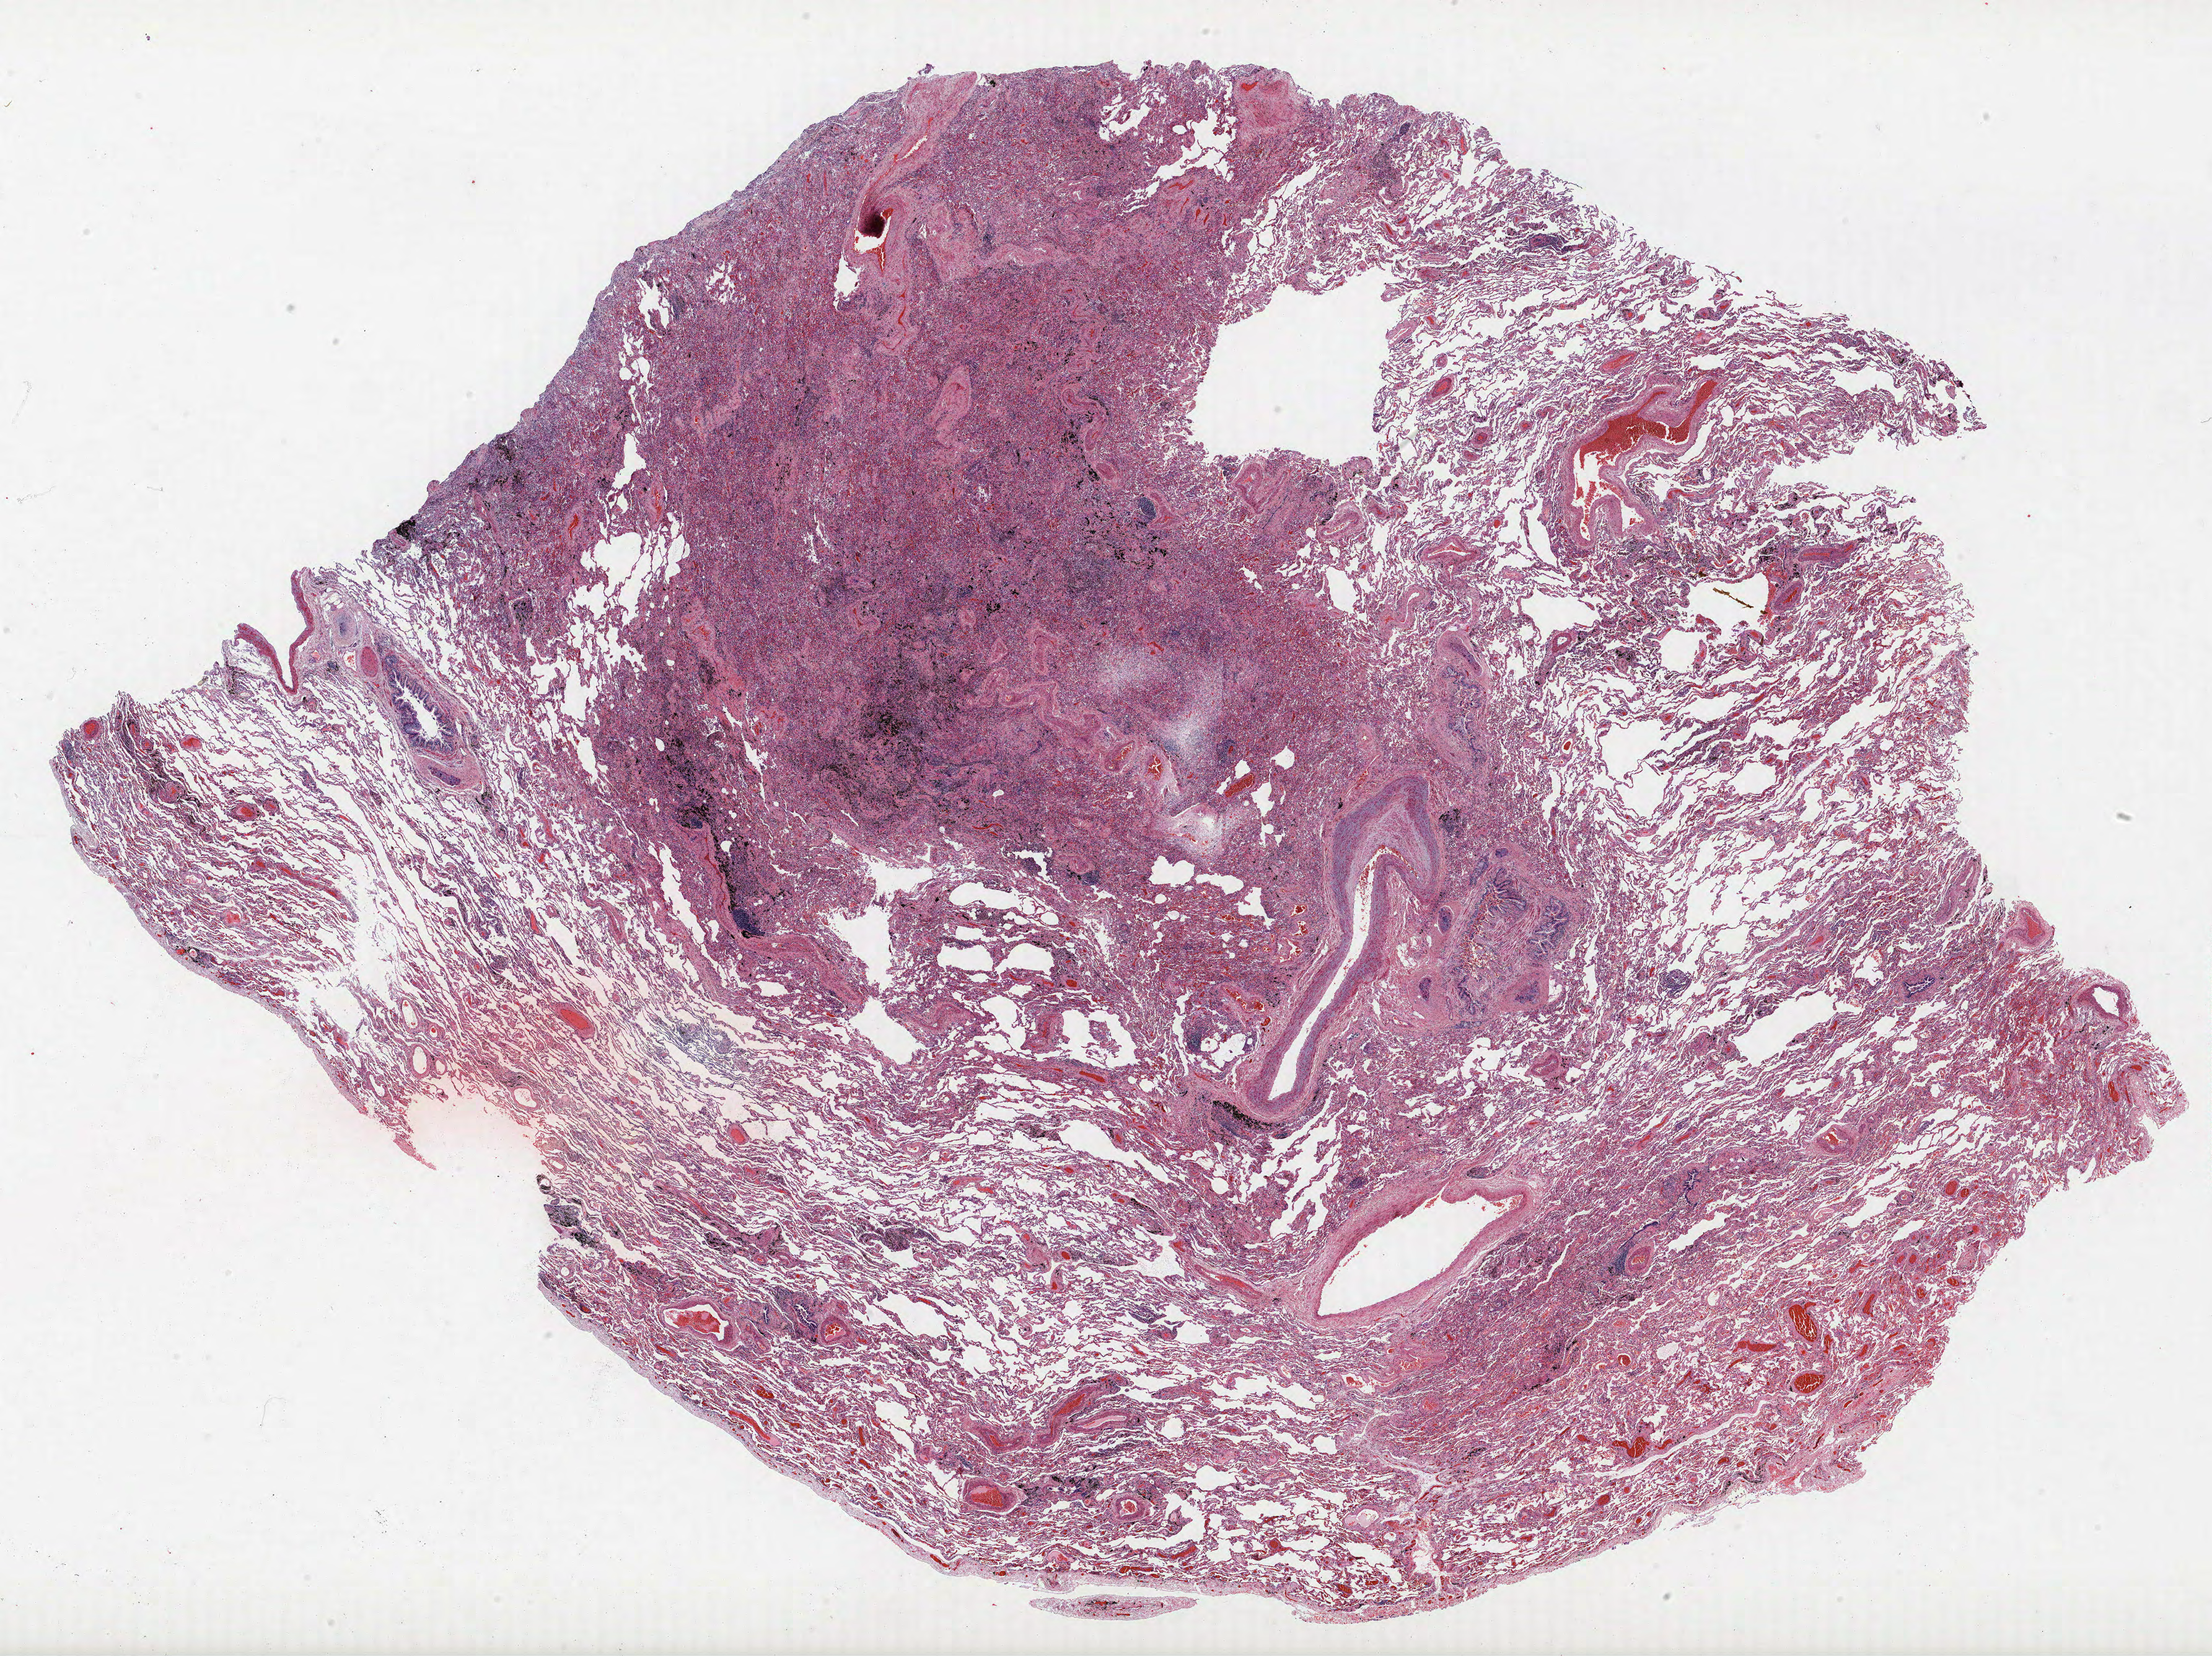
Whole-slide histology image, H&E, low-resolution overview of the scanned area, about 28.6 x 21.4 mm; FFPE section; lung. Male, age 66 at enrolment. Grade: poorly differentiated (G3).
Tumour size (pathology): 30 mm. Stage (AJCC 6th edition): IB. Primary tumour location (clinical record): left upper lobe. Participant's lung-cancer diagnosis: Squamous cell carcinoma, NOS (ICD-O-3 8070/3).